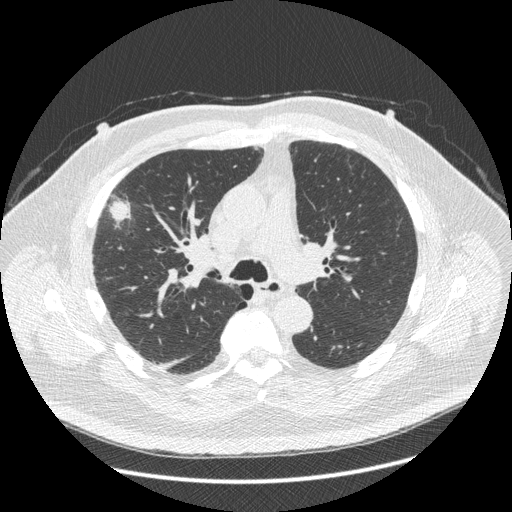
Low-dose screening chest CT, axial slice. Third screening round (two years after baseline). Lung window (W 1500 / L -600 HU). Standard (soft-tissue) reconstruction kernel (STANDARD). Slice 154 of 426 in the series. 512 × 512 image matrix, field of view 400 × 400 mm. Male, age 66 years at enrolment. Current smoker at enrolment.
- Expert-annotated lung lesion, bounding box (x1, y1, x2, y2) in pixels: (86, 179, 145, 264).
- Screening reader's record for this exam (one nodule recorded; not confirmed to be the boxed lesion): non-calcified nodule or mass ≥4 mm, right upper lobe, 48 × 25 mm, spiculated (stellate) margins, soft tissue attenuation, pre-existing on the prior screen: no.
- Later outcome: lung cancer diagnosed 35 days after this screen — non-small cell carcinoma, right upper lobe, stage IV (AJCC 6th edition), 50 mm at pathology.